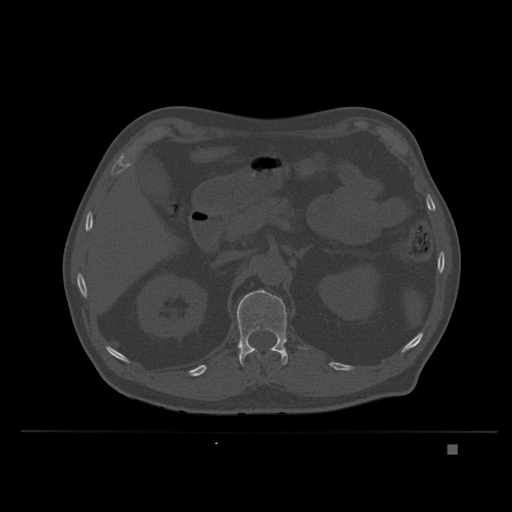
CT including the spine, one axial slice; slice 143 of 435 in the series (ordered by position); bone window (W 1800 / L 400 HU); 512 × 512 image matrix, field of view 434 × 434 mm. Male patient, age 73 years. Case-level facts recorded for this patient, not image findings: primary cancer: skin.
Outlined on this slice (semi-automatic segmentation, software-assisted and operator-edited):
- L1 vertebra: box from (x=237, y=290) to (x=307, y=366) px
- T12 vertebra: (x=250, y=350)–(x=255, y=354)